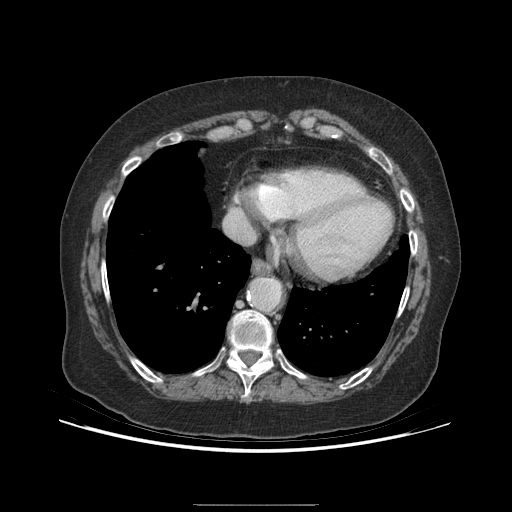
Contrast-enhanced abdominal CT (liver protocol), one axial slice; slice 186 of 192 in the series (ordered by position); 140 kVp; soft-tissue window (W 400 / L 40 HU); 2.5 mm slice thickness; 512 × 512 image matrix, field of view 400 × 400 mm. Case-level facts recorded for this patient, not image findings: diagnosis: hepatocellular carcinoma (patient treated with transarterial chemoembolisation; whether this scan precedes or follows treatment is not stated here); TNM stage (as recorded): Stage-I; Child-Pugh class: A; tumour nodularity: uninodular; tumour size: 3.2 cm.
Structures marked on this image (semi-automatically segmented with operator editing):
- abdominal aorta: box from (x=251, y=280) to (x=279, y=308) px